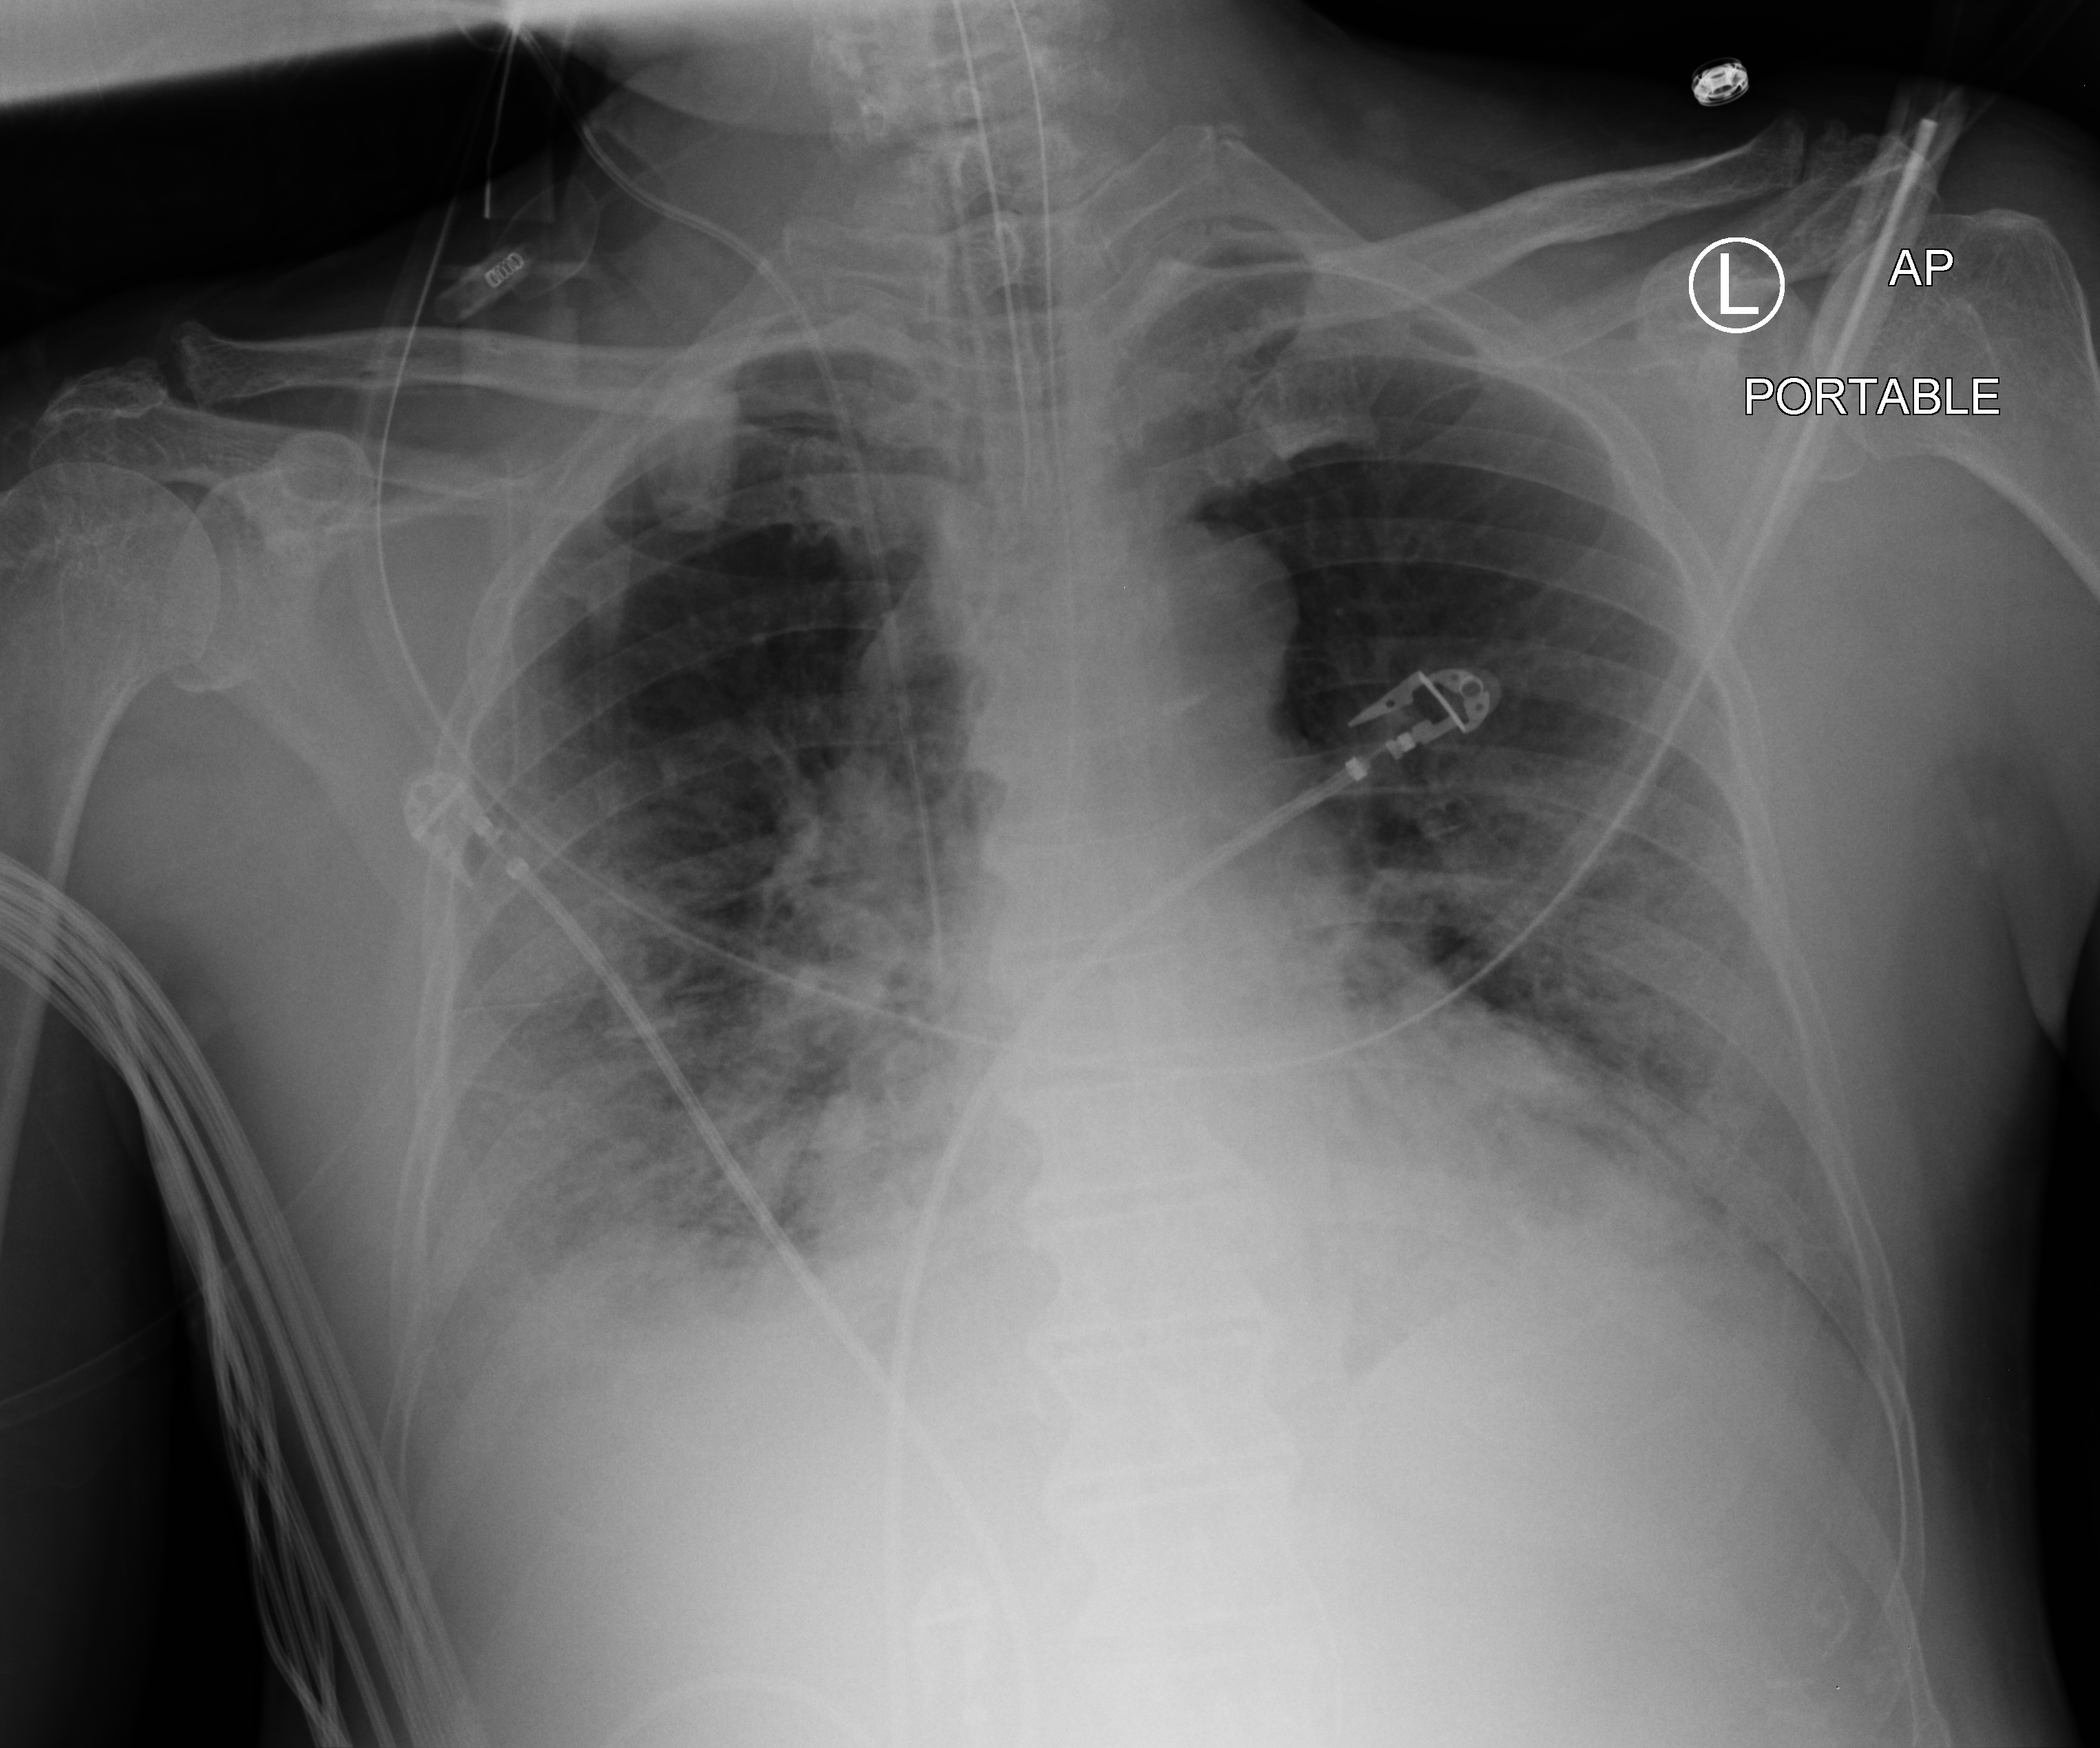
Bedside chest radiograph (computed radiography), anteroposterior (AP) projection. Patient hospitalised with COVID-19; male, aged 60–74 years.
Hospital-stay facts (about this admission, not read from this image; timing relative to this image not recorded): mechanically ventilated during this hospital stay: yes.